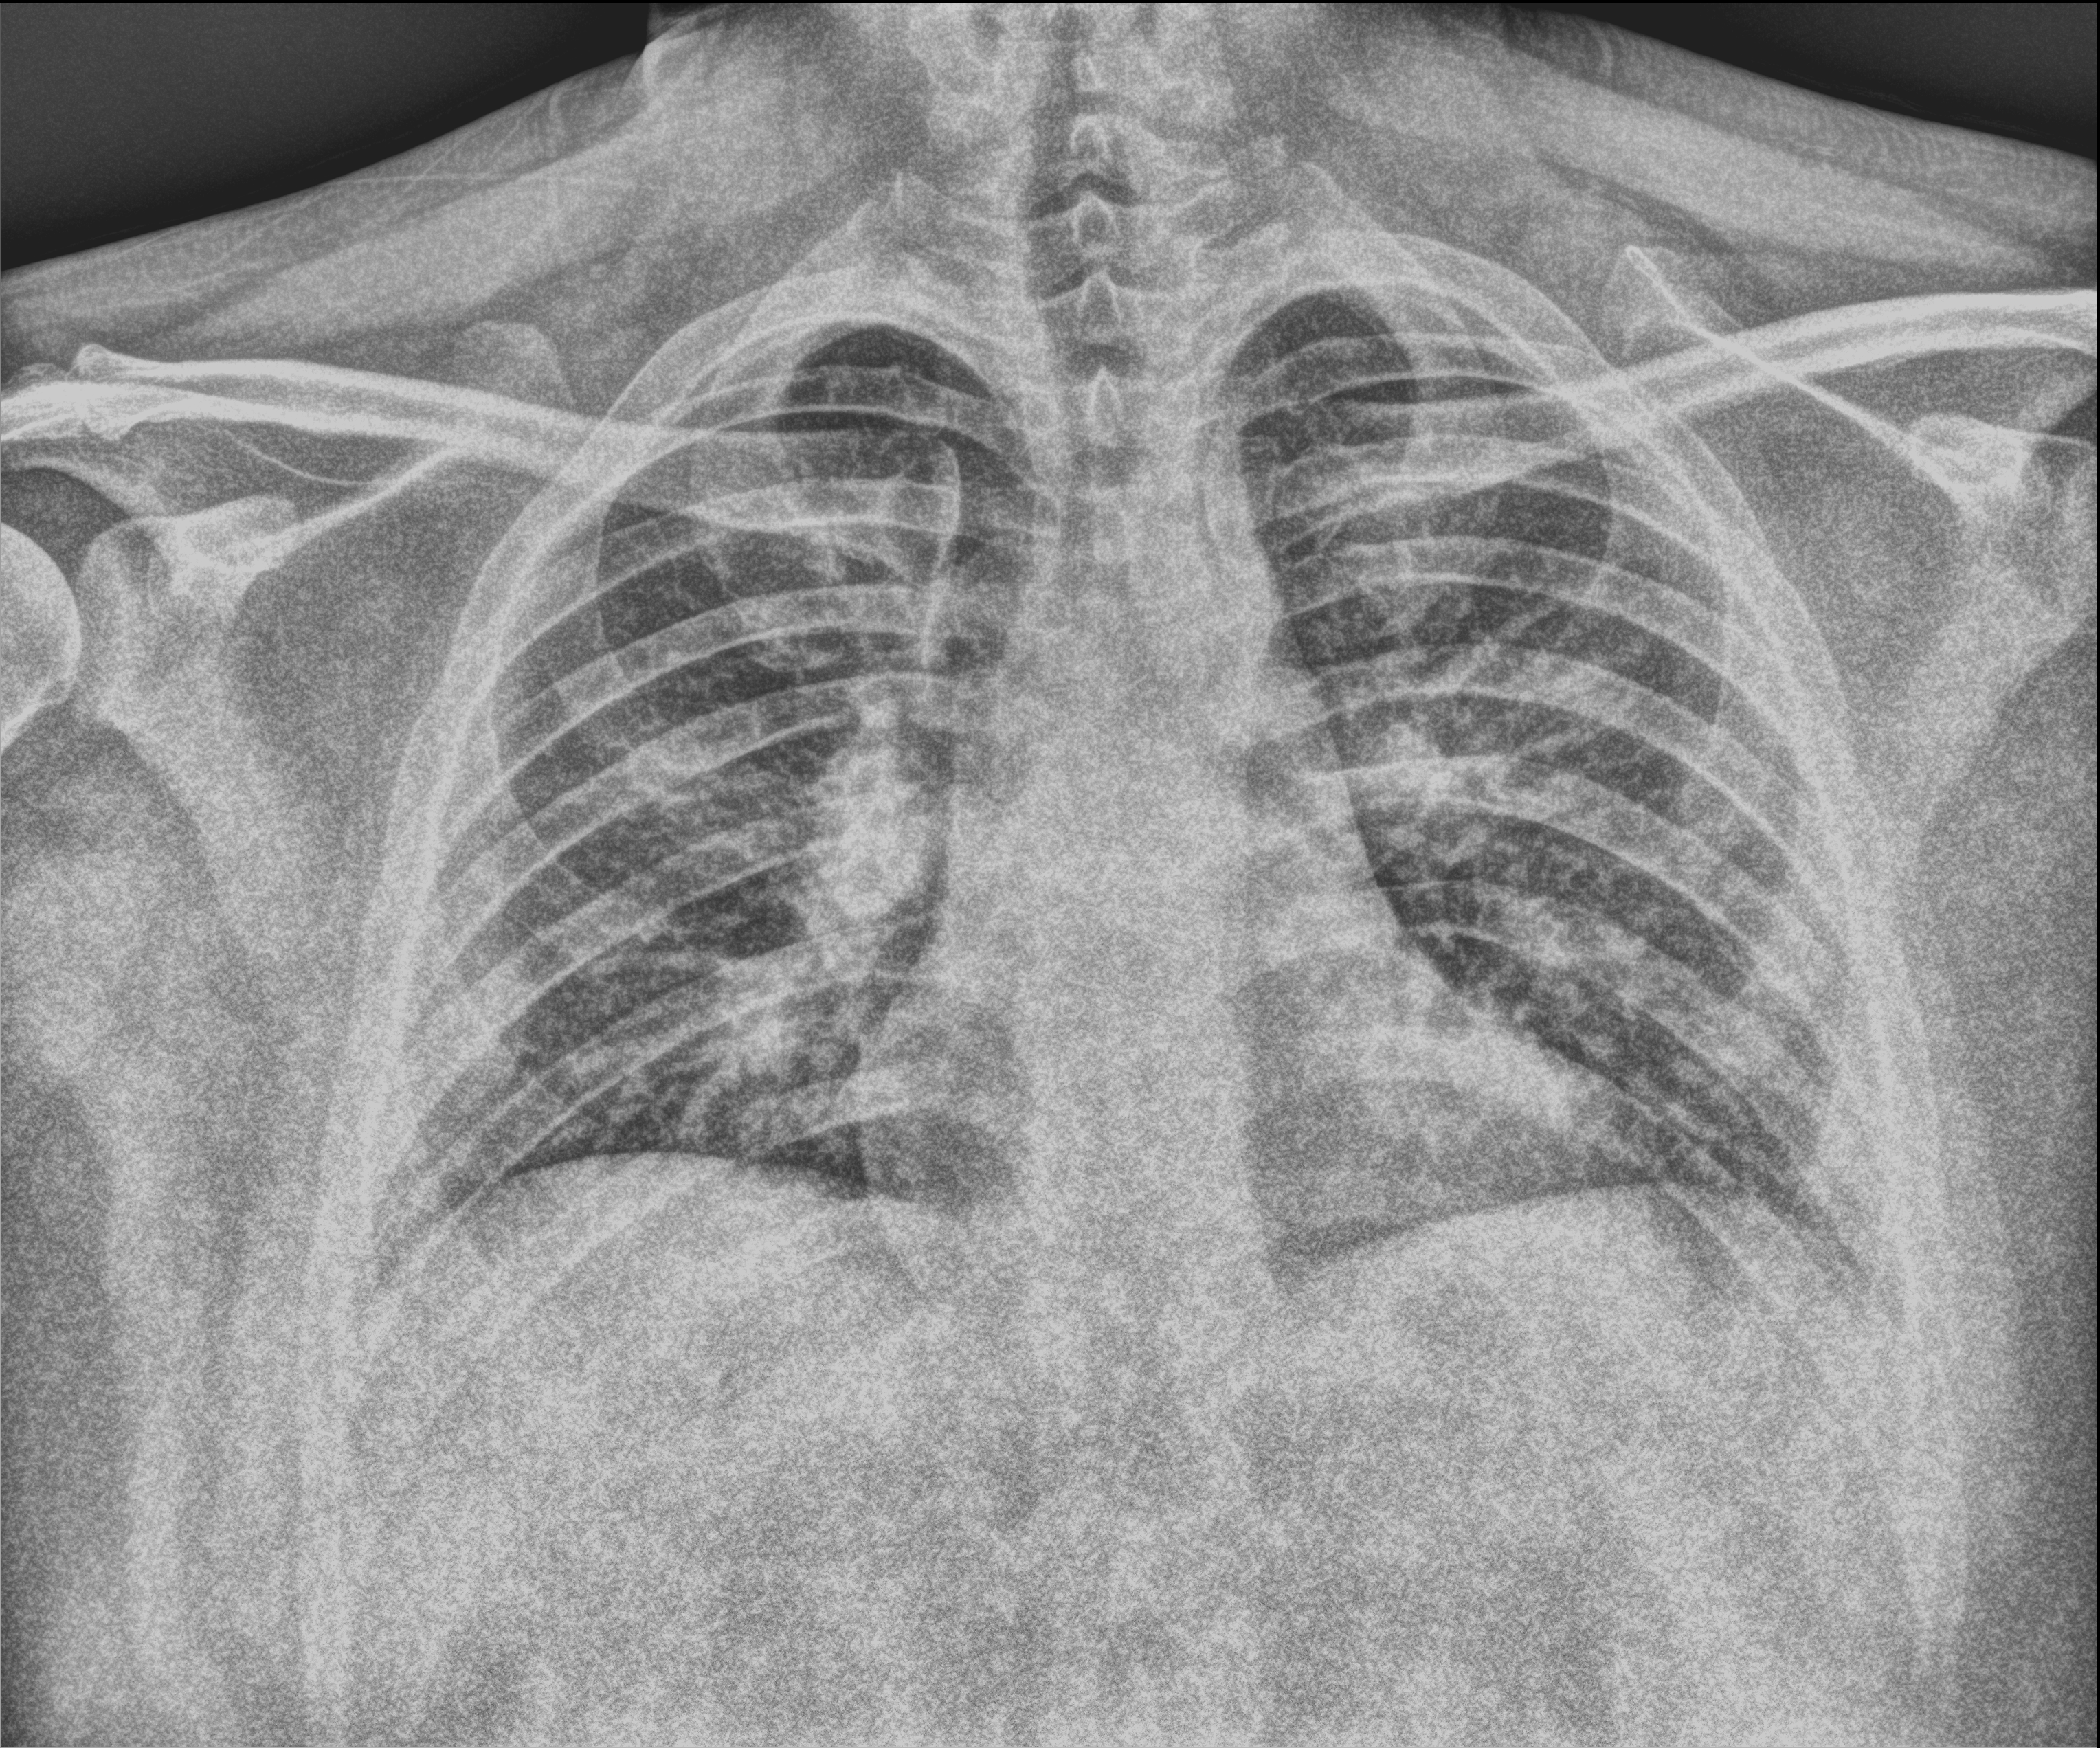
Chest X-ray (portable); anteroposterior (AP) projection. Male patient hospitalised with COVID-19, age 18–59 years.
Hospital-stay facts (about this admission, not read from this image; timing relative to this image not recorded):
- length of hospital stay: 11 days
- admitted to intensive care during this hospital stay: no